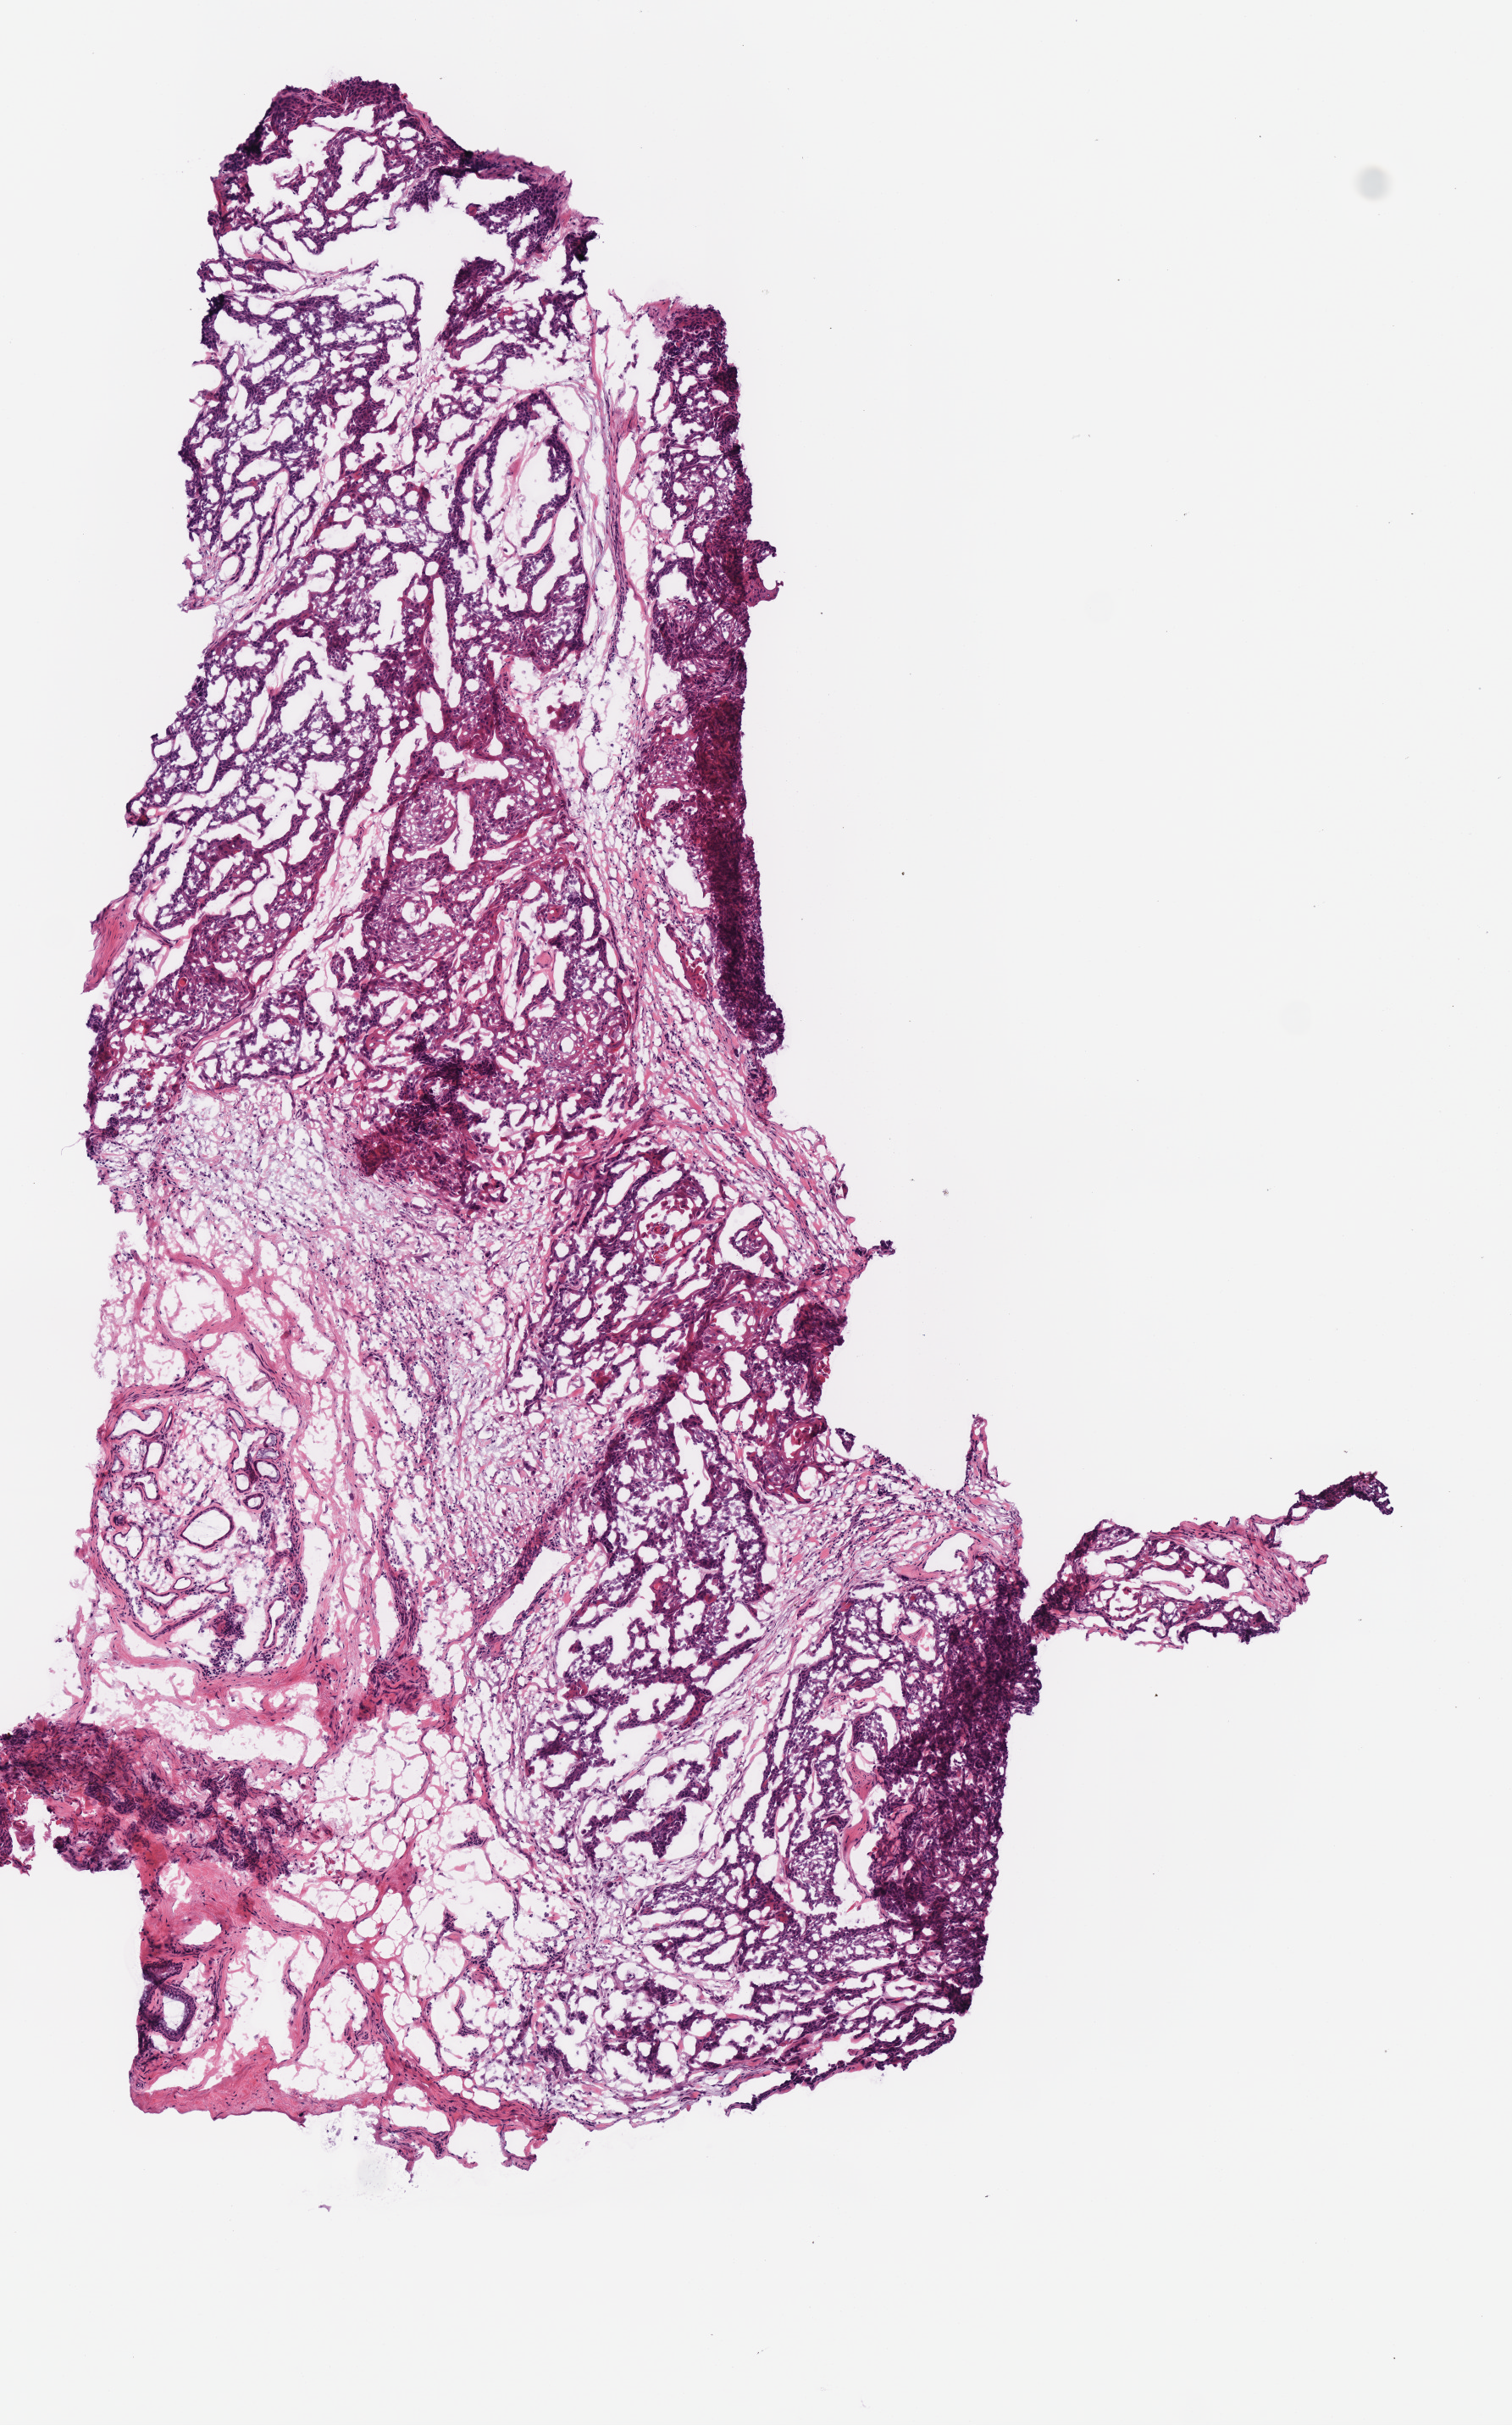
Digitized H&E tissue section (whole slide), shown as a low-resolution overview of the whole scanned area (about 3.5 x 5.6 mm), frozen section from the top of the tissue portion, primary tumour sample from the head and neck. Male, age 66 years at initial diagnosis. Histologic grade: G2 (moderately differentiated). Composition of this section per pathologist review: tumour cells 70%, tumour nuclei 75%, normal cells 0%, stromal cells 30%, necrosis 0%.
AJCC pathologic stage: IVA. Pathologic diagnosis: Squamous cell carcinoma, NOS. TNM: T2 N2b.